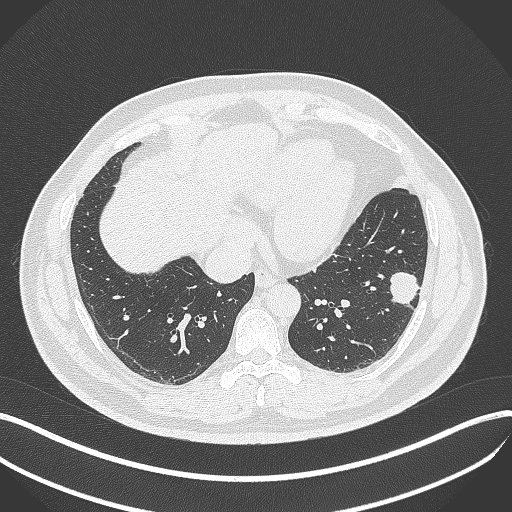
Chest CT, one axial slice. Position 138 of 429 along the scan axis. Reconstruction kernel B70f. 120 kVp. Lung window (W 1500 / L -600 HU). 1 mm slice thickness. 512 × 512 image matrix, field of view 400 × 400 mm. Male patient, age 39 years. Case-level facts recorded for this patient, not image findings: clinical TNM (as recorded): T2a N0 M0.
Outlined on this slice (rectangle marked by the reading radiologist):
- lung tumour (recorded histology: adenocarcinoma): bounding box <388,268,422,307> (left, top, right, bottom; pixels)